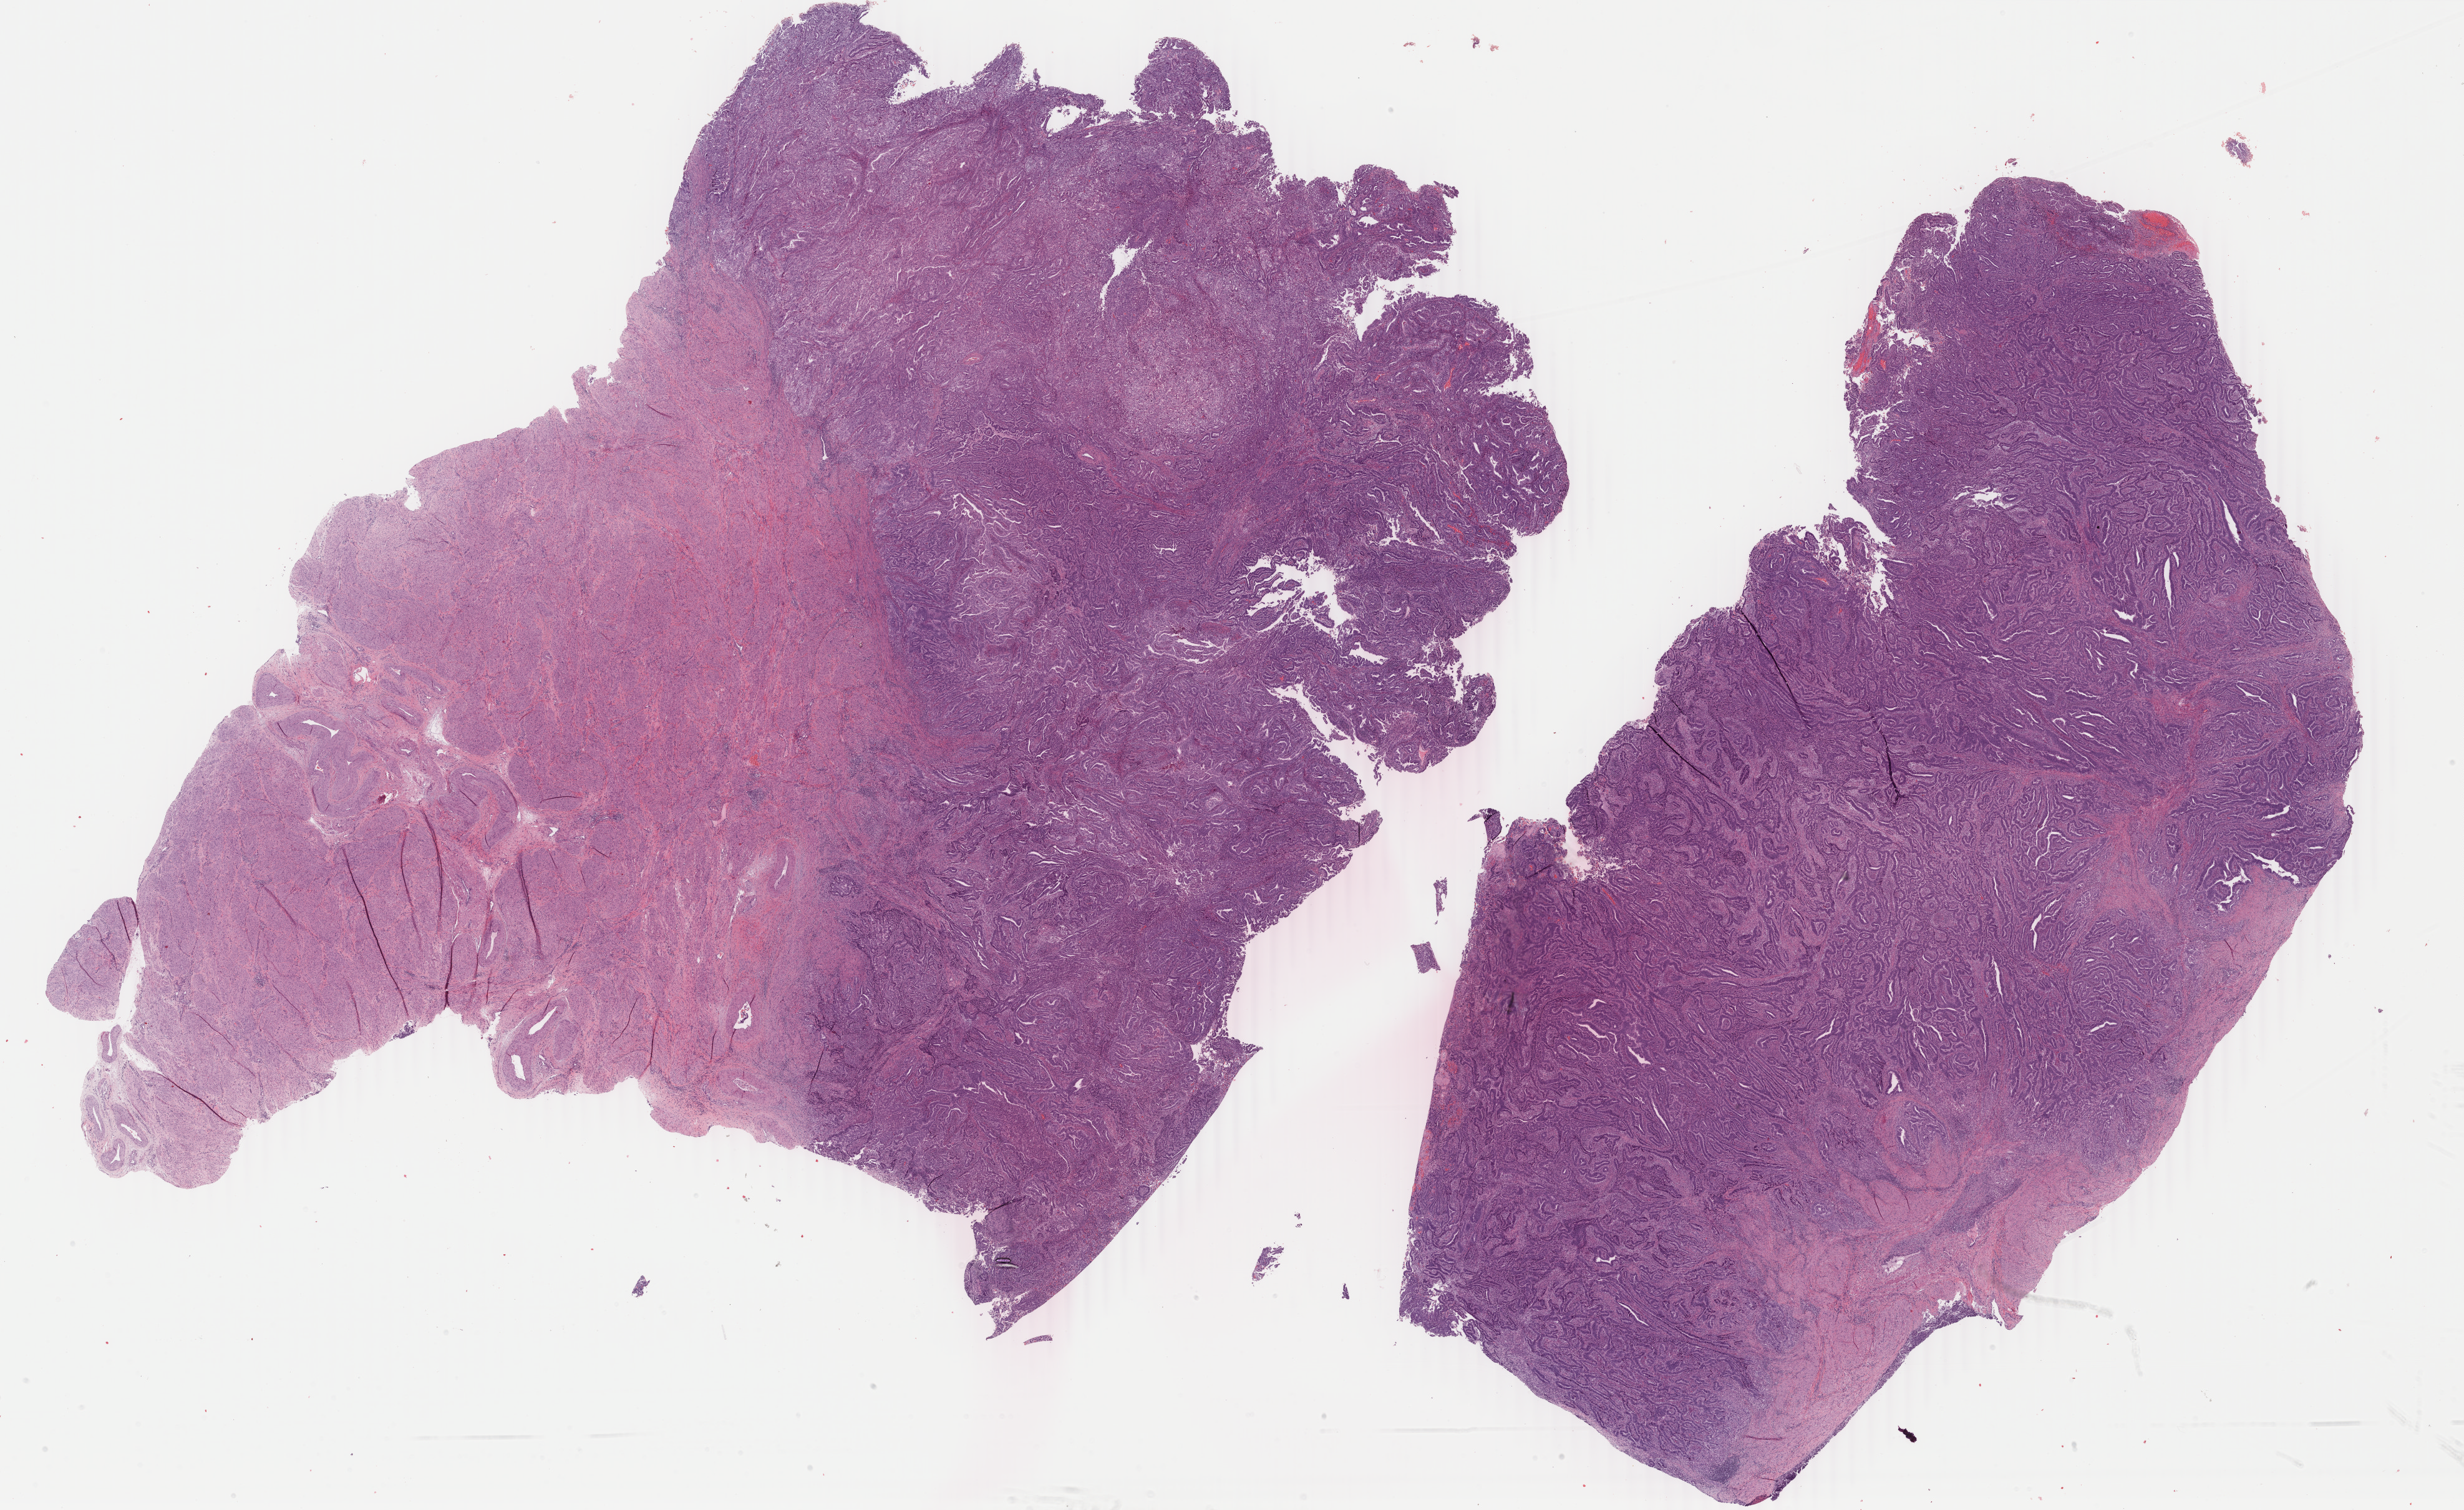
Digitized Hematoxylin and eosin (H&E) stained tissue section (whole slide), a low-resolution overview of the entire scanned area, about 31.4 x 19.2 mm (from a 40x scan); FFPE section; sample: primary tumour, uterus. Female, age 55 years at initial diagnosis. Histologic grade: G3 (poorly differentiated).
Pathologic diagnosis: Endometrioid adenocarcinoma, NOS (endometrium). FIGO stage: IIB.